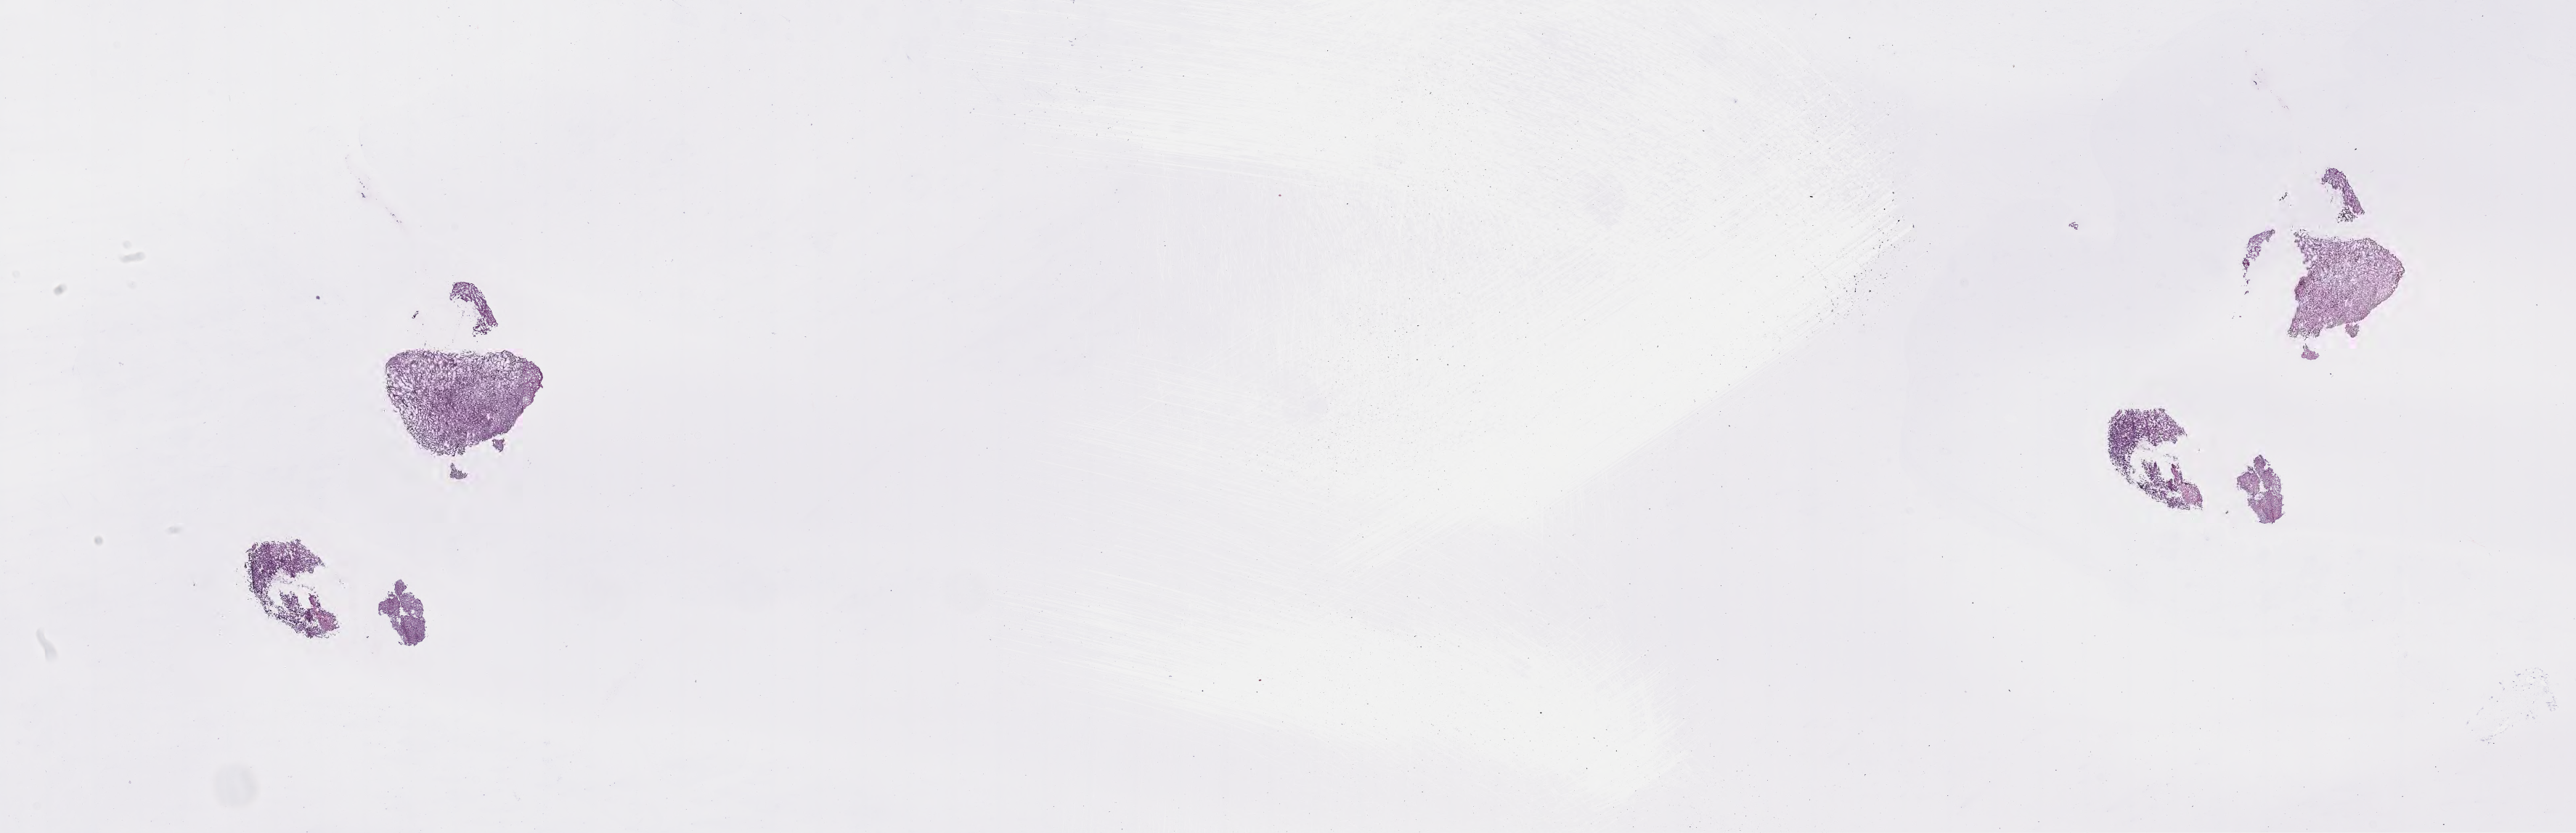
Digitized H&E-stained section of tumor tissue from the brain — low-resolution overview of the scanned area, about 28.7 x 9.3 mm, cryosection (OCT / tissue freezing medium). Patient: male, age 138 months (11 years 6 months).
* diagnosis: Neoplasm, malignant